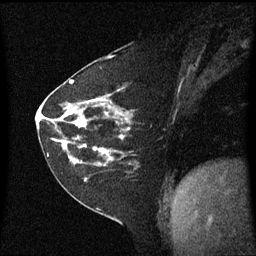
Breast MRI (dynamic contrast-enhanced), one sagittal slice. Slice 28 of 60 in the series (ordered by position). Dynamic contrast-enhanced series, image 2 of 3 at this slice position (ordered by acquisition). 1.5 T. TE 4.2 ms, TR 8.4 ms. 256 × 256 image matrix, field of view 210 × 210 mm. Female patient, age 60 years. Case-level facts recorded for this patient, not image findings: setting: breast cancer imaged before/during neoadjuvant chemotherapy; receptor status: triple-negative.
Annotated regions visible in this slice (semi-automatically segmented with operator editing):
- analysis volume of interest (the breast-tissue region the enhancement analysis was run in; not a lesion): bounding box <45,99,138,182> (left, top, right, bottom; pixels)
- tumour enhancement mask (voxels above the 70 % enhancement threshold inside the analysis volume of interest): <48,100,129,161>